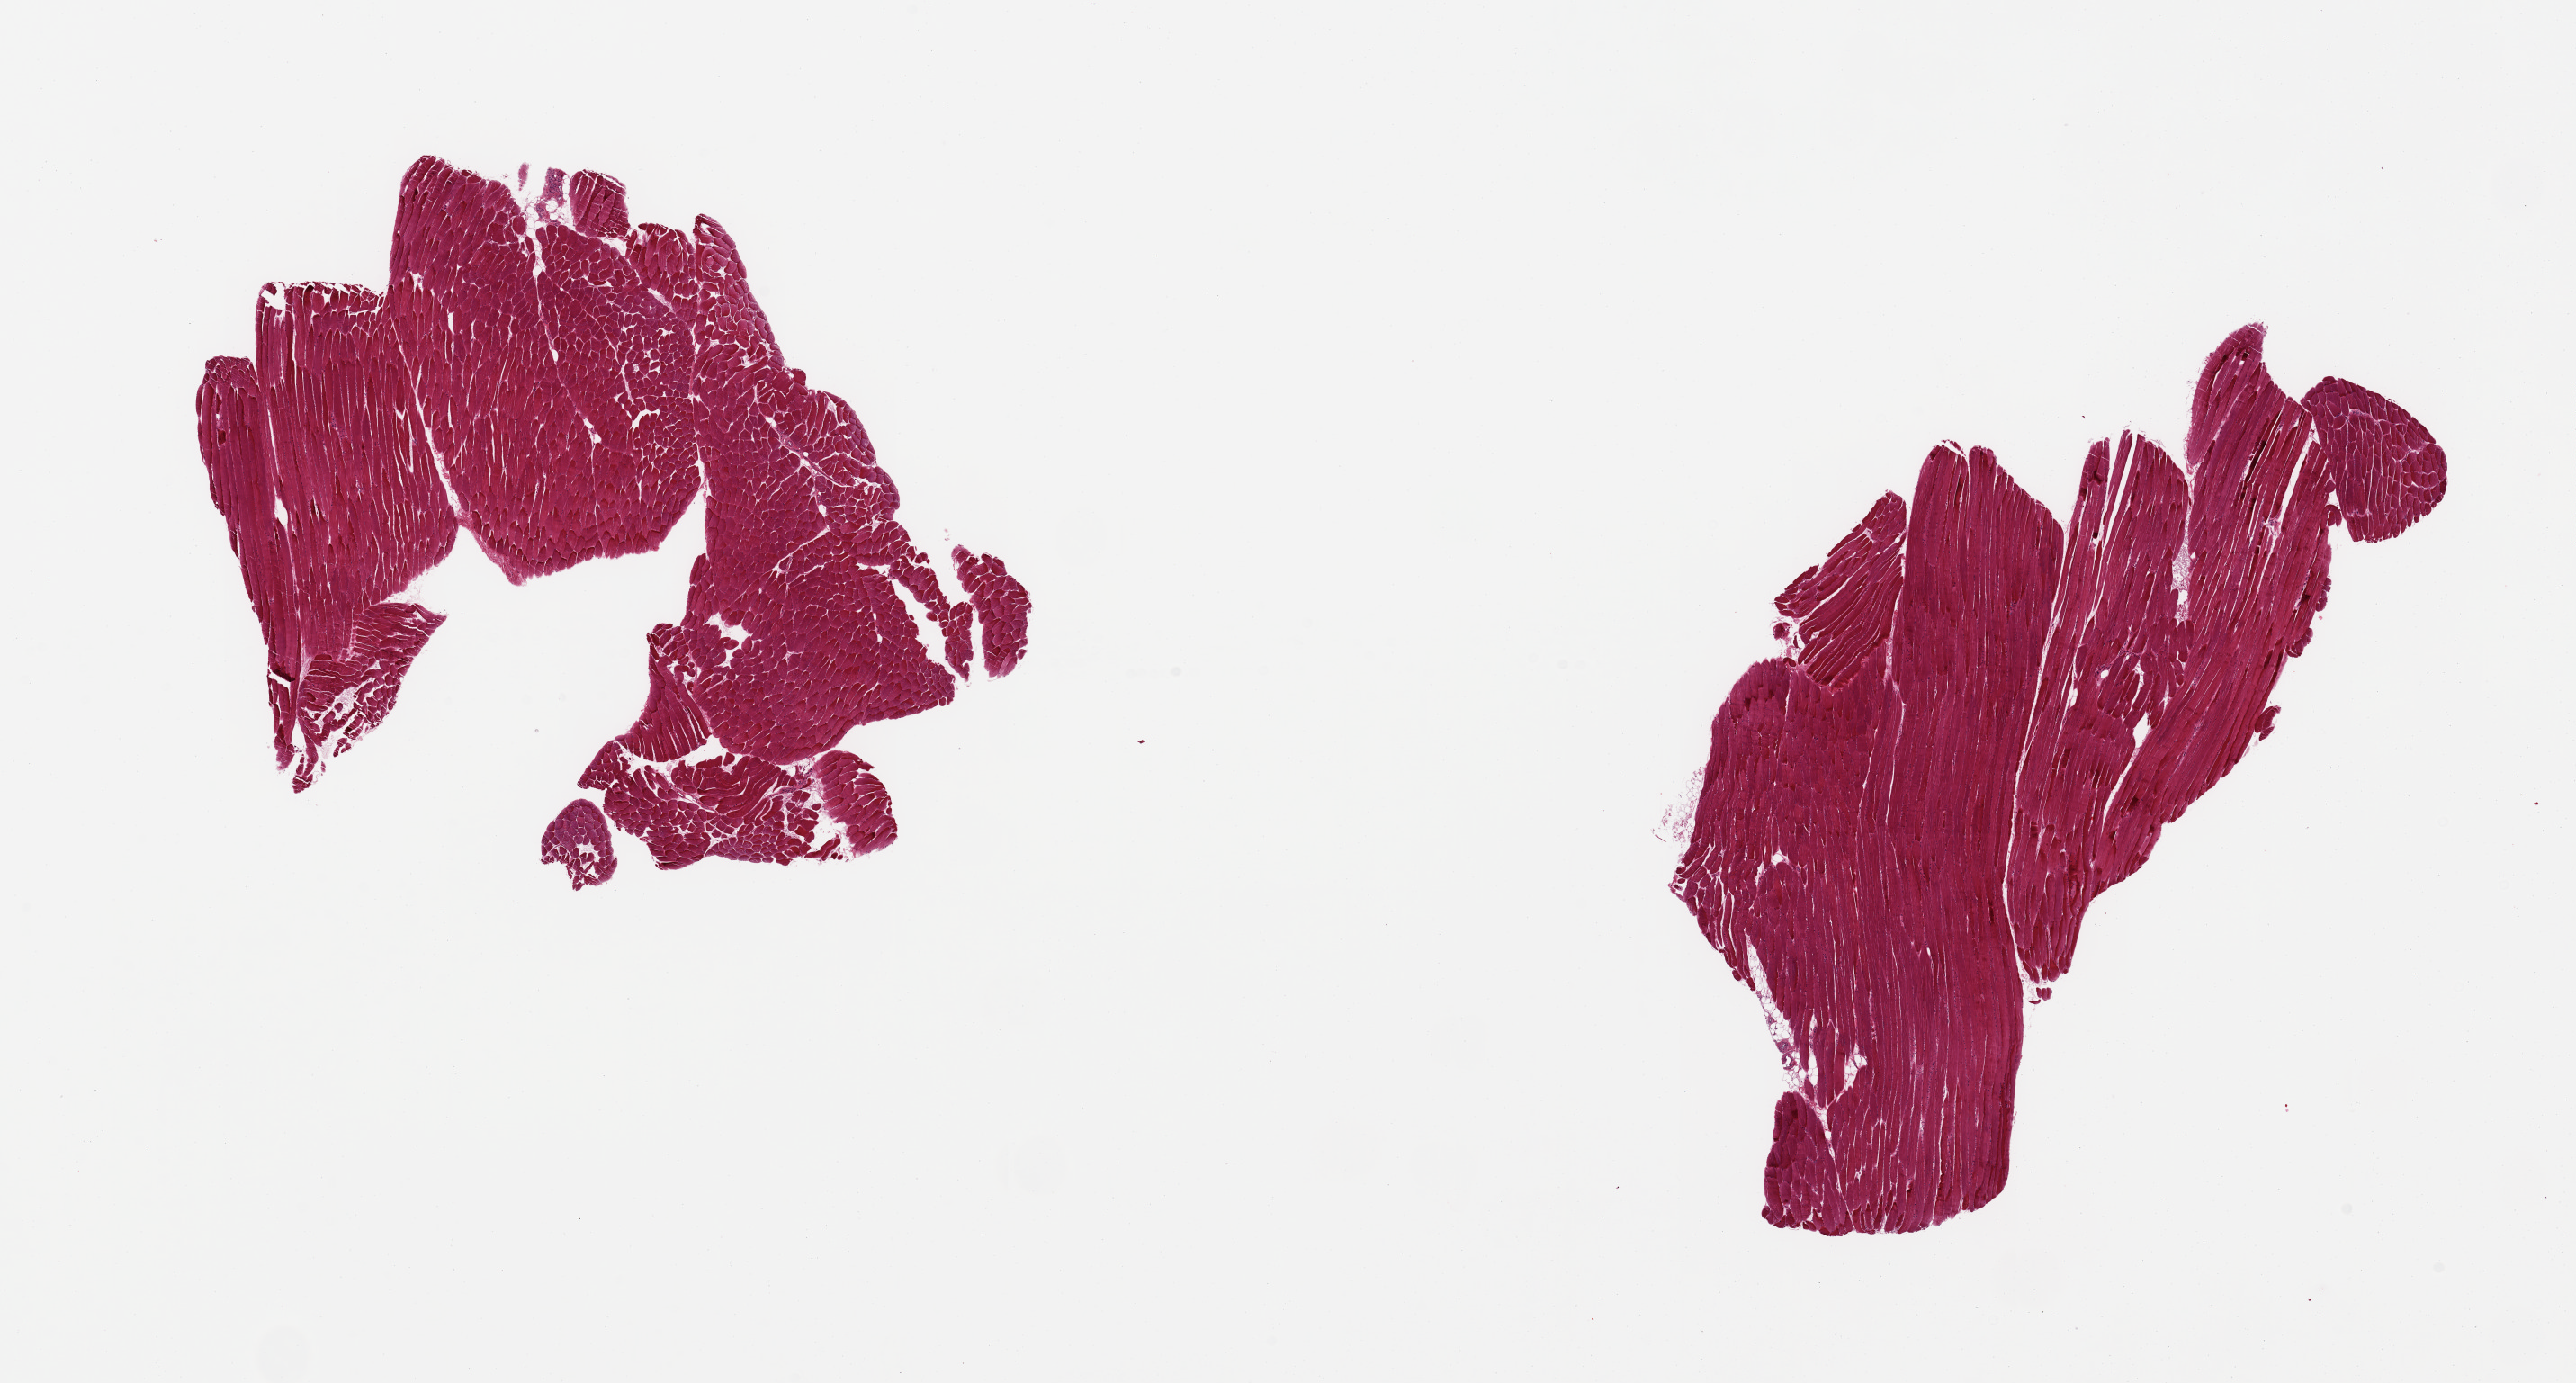
Whole-slide image, H&E stain, brightfield, shown as a low-resolution overview of the whole scanned area (about 22.6 x 12.2 mm); PAXgene-fixed paraffin-embedded (PFPE) section; section of skeletal muscle (target tissue); donor tissue sample. Donor sex: male.
Pathologist's review note for this sample: 2 pieces, minimal interstitial fat.